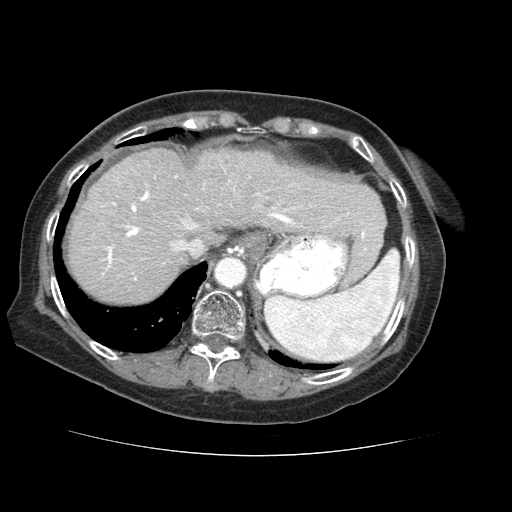
Contrast-enhanced abdominal CT (liver protocol), one axial slice. Slice 51 of 73 in the series (ordered by position). Reconstruction kernel STANDARD. 120 kVp. Soft-tissue window (W 400 / L 40 HU). 512 × 512 image matrix, field of view 360 × 360 mm. From the clinical record (not read from this slice): diagnosis: hepatocellular carcinoma (patient treated with transarterial chemoembolisation; whether this scan precedes or follows treatment is not stated here); TNM stage (as recorded): Stage-IVB; Child-Pugh class: A; tumour differentiation: well differentiated; tumour nodularity: uninodular.
Annotated regions visible in this slice (semi-automatic segmentation, software-assisted and operator-edited):
- abdominal aorta: bounding box [x1, y1, x2, y2] px = [217, 258, 247, 286]
- liver parenchyma outside the tumour (the mass and vessels are separate outlines, so this box may not span the whole liver): [68, 148, 382, 302]
- mass: [196, 150, 231, 179]
- liver vessels: [102, 176, 349, 280]